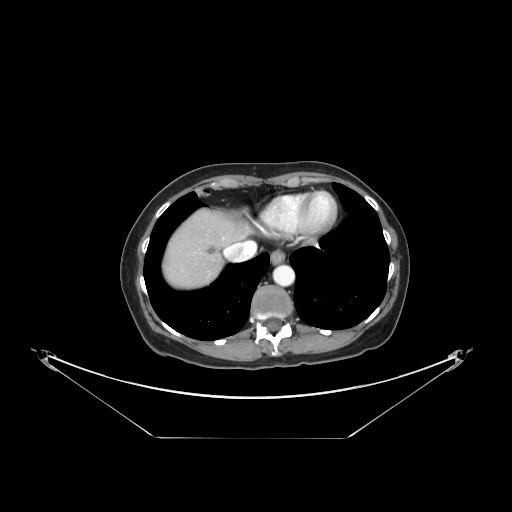
Contrast-enhanced abdominal CT, one axial slice; position 133 of 148 along the scan axis; reconstruction kernel STANDARD; 120 kVp; intravenous contrast given; soft-tissue window (W 400 / L 40 HU); 512 × 512 image matrix, field of view 500 × 500 mm. Female patient, age 73 years. From the clinical record (not read from this slice): diagnosis: colorectal cancer liver metastases, imaged before liver resection; multiple liver metastases: no; largest metastasis: 1 cm; chemotherapy before resection: yes.
Structures marked on this image (manually delineated by an expert):
- liver: bounding box <163,212,243,287> (left, top, right, bottom; pixels)
- planned liver remnant (the part of the liver to remain after resection): <194,212,244,242>
- liver metastasis: <206,245,218,258>